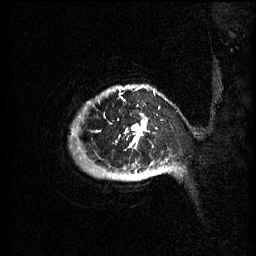
Breast MRI (dynamic contrast-enhanced), one sagittal slice. Position 56 of 60 along the scan axis. 3 images stored at this slice position (order not interpretable as contrast timing). 1.5 T. TE 4.2 ms, TR 11 ms. 2 mm slice thickness. 256 × 256 image matrix, field of view 220 × 220 mm. Female patient, age 51 years.
Annotated regions visible in this slice (semi-automatically segmented with operator editing):
- analysis volume of interest (the breast-tissue region the enhancement analysis was run in; not a lesion): box from (x=80, y=86) to (x=176, y=181) px
- tumour enhancement mask (voxels above the 70 % enhancement threshold inside the analysis volume of interest): (x=119, y=86)–(x=167, y=179)